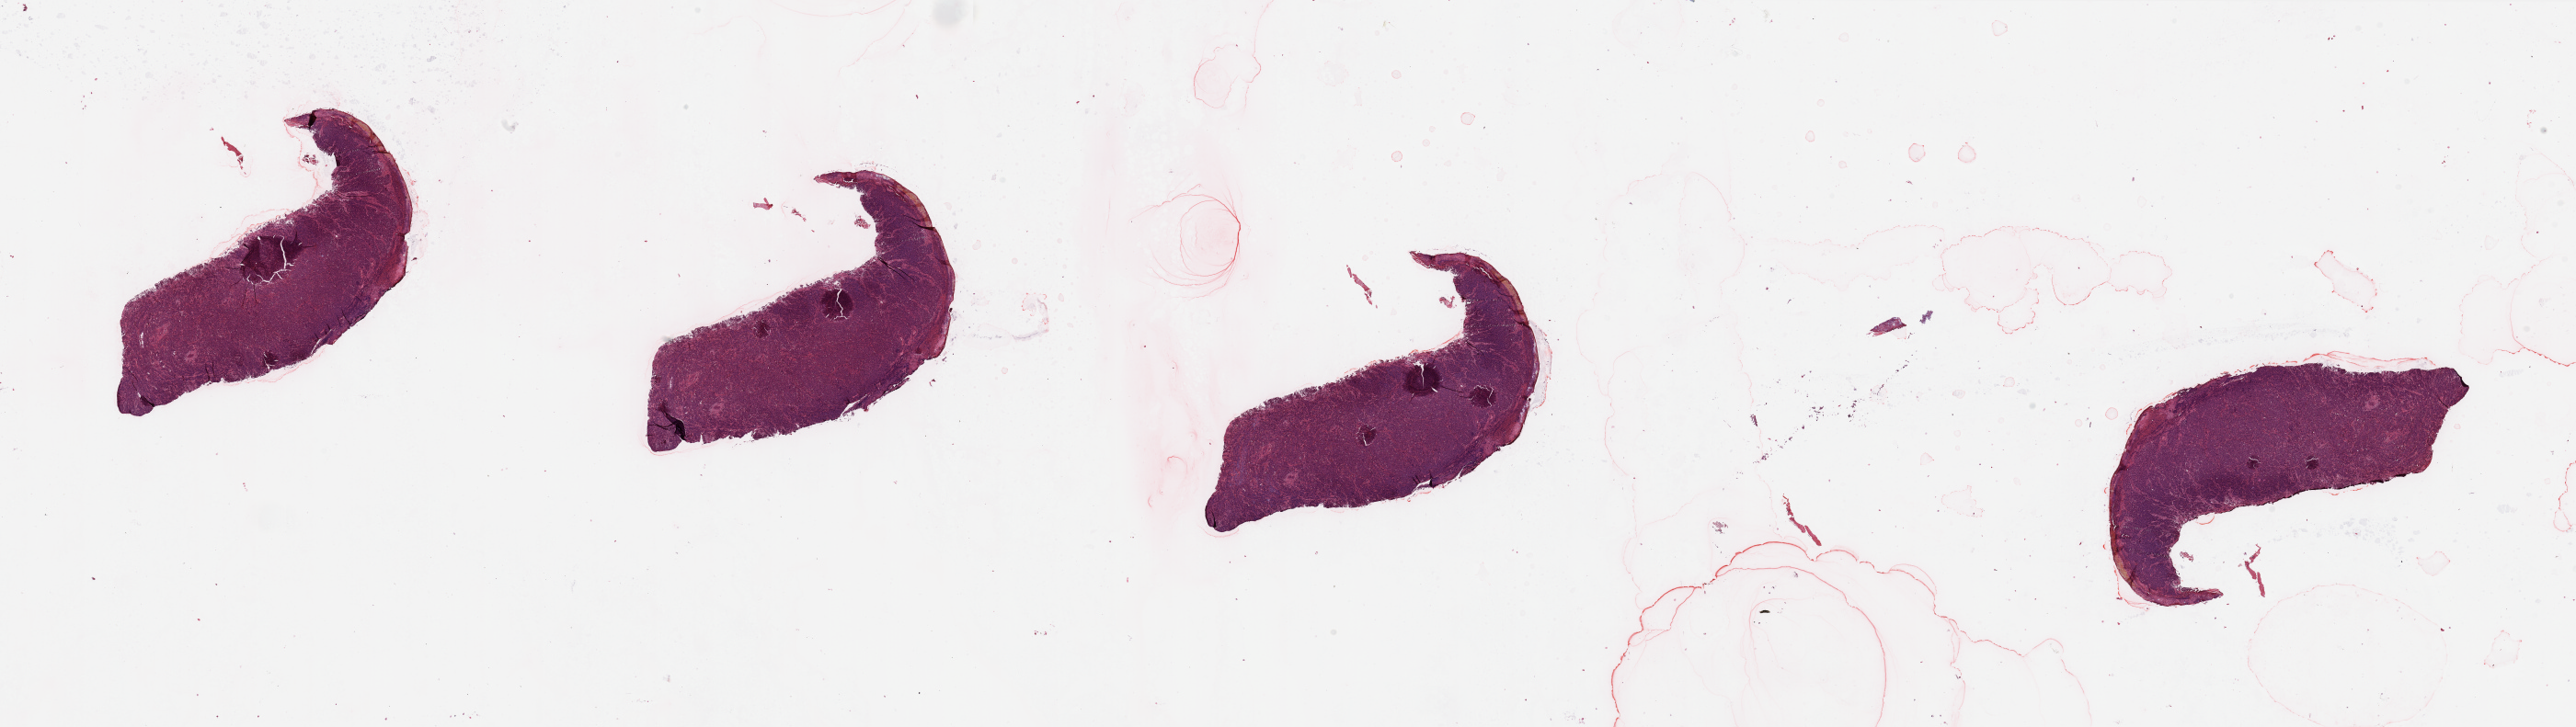
Digitized H&E-stained tissue section (whole slide) — whole scanned area (about 44.3 x 12.5 mm, slide scanned at 20x) shown as a low-resolution overview; melanoma tumour tissue; sampled site not recorded. Male, 42 y/o.
• diagnosis: Malignant melanoma, NOS
• AJCC pathologic stage: IIC
• primary tumour site (as recorded): trunk